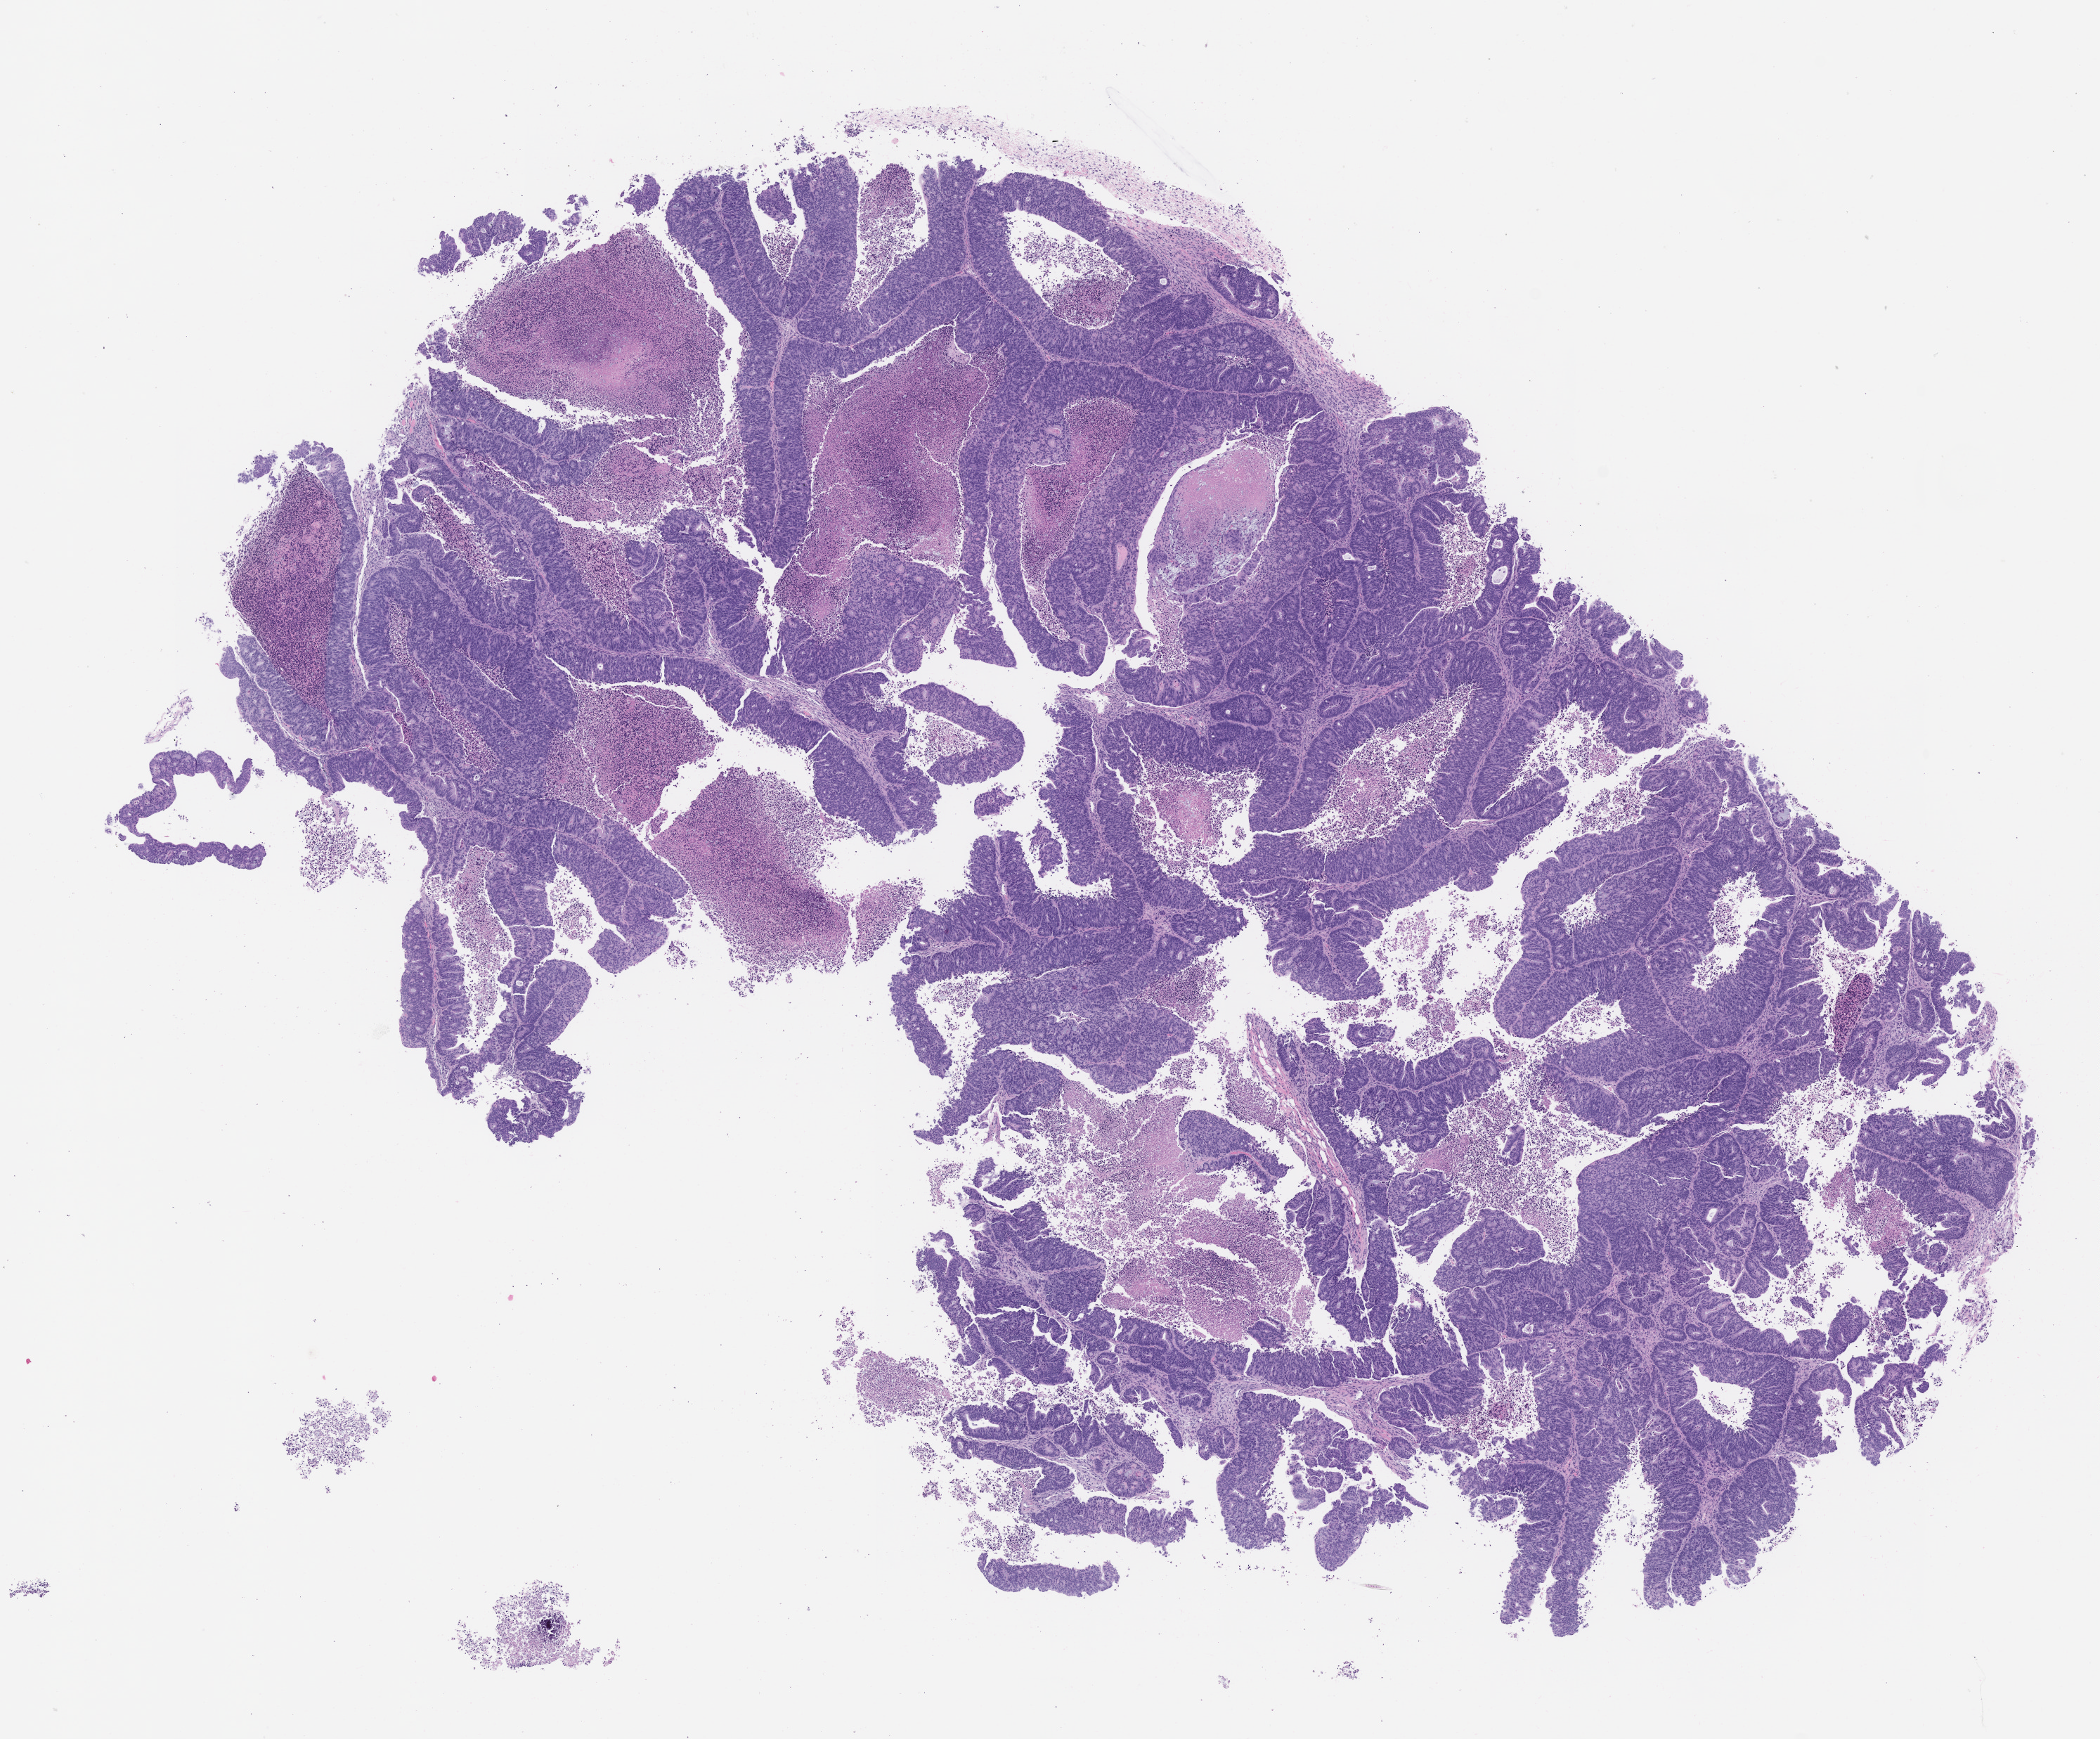
Whole-slide image, haematoxylin and eosin: patient-derived xenograft (human tumor grown in a mouse), passage 2, a low-resolution overview of the entire scanned area, about 12.0 x 9.9 mm; FFPE section; tumor site category: colon.
Originating patient diagnosis: Colon Adenocarcinoma.